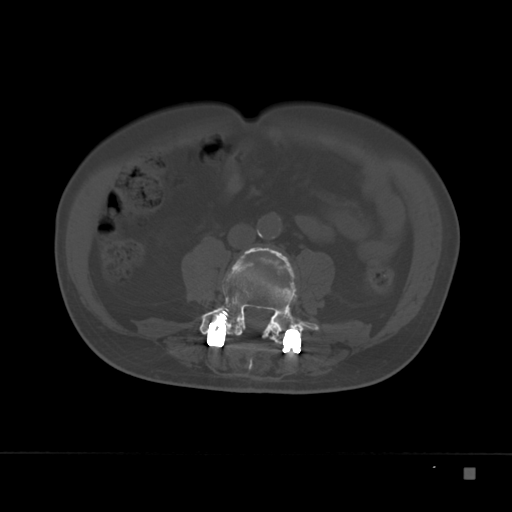
CT including the spine, one axial slice; position 52 of 332 along the scan axis; reconstruction kernel Br40s; 120 kVp; bone window (W 1800 / L 400 HU); 512 × 512 image matrix. Male patient, age 72 years. Case-level facts recorded for this patient, not image findings: primary cancer: skeletal.
Outlined on this slice (semi-automatic segmentation, software-assisted and operator-edited):
- L3 vertebra: bounding box (x1, y1, x2, y2) in pixels: (241, 247, 296, 294)
- L4 vertebra: (200, 250, 319, 344)